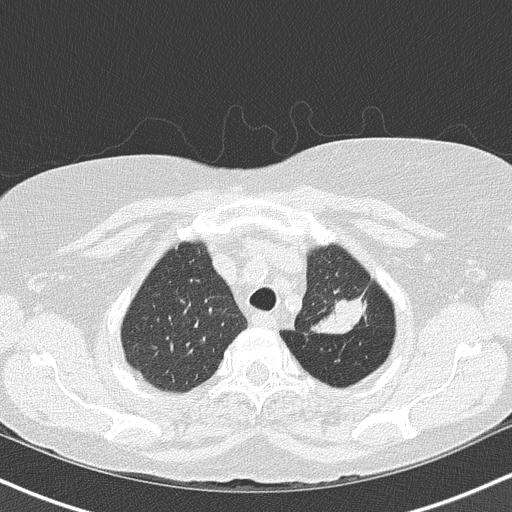
Low-dose screening chest CT, one axial slice. Position 125 of 147 along the scan axis. Reconstruction kernel B50f. Lung window (W 1500 / L -600 HU). 2 mm slice thickness. 512 × 512 image matrix, field of view 320 × 320 mm.
Annotated regions visible in this slice (outlined manually by an expert reader):
- lesion 1 (tumor, upper lobe of left lung): bounding box <313,299,365,334> (left, top, right, bottom; pixels)